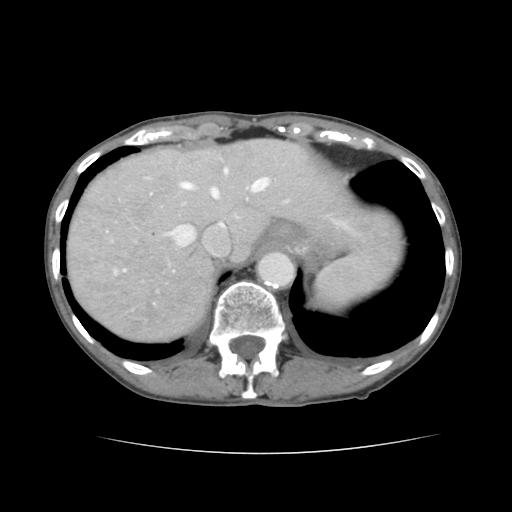
Contrast-enhanced abdominal CT, one axial slice; slice 115 of 136 in the series (ordered by position); 120 kVp; intravenous contrast given; soft-tissue window (W 400 / L 40 HU); 512 × 512 image matrix, field of view 319 × 319 mm. Female patient, age 77 years. From the clinical record (not read from this slice): diagnosis: colorectal cancer liver metastases, imaged before liver resection; multiple liver metastases: yes; largest metastasis: 3 cm; chemotherapy before resection: yes.
Outlined on this slice (outlined manually by an expert reader):
- hepatic veins: bounding box (x1, y1, x2, y2) in pixels: (134, 169, 268, 256)
- liver: (67, 139, 396, 341)
- planned liver remnant (the part of the liver to remain after resection): (171, 139, 399, 257)